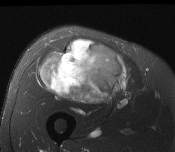
MRI of an extremity soft-tissue mass, one axial slice. Position 83 of 116 along the scan axis. T2-weighted fat-saturated. MR volume resampled by the dataset authors to the PET/CT grid (not the native acquisition matrix). 3.27 mm slice thickness. 175 × 152 image matrix, field of view 171 × 148 mm. Male patient. From the clinical record (not read from this slice): histological type: pleiomorphic leiomyosarcoma; grade: intermediate; site of the primary tumour: right thigh.
Outlined on this slice (expert contour drawn on MRI and transferred to this co-registered scan by the dataset authors):
- gross tumour volume including surrounding oedema: bounding box (x1, y1, x2, y2) in pixels: (40, 40, 128, 103)
- gross tumour volume (mass): (40, 40, 128, 103)